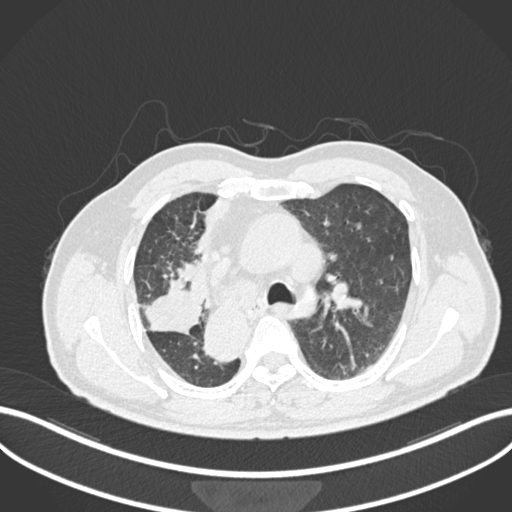
Chest CT, one axial slice; 120 kVp; lung window (W 1500 / L -600 HU); 1 mm slice thickness; 512 × 512 image matrix, field of view 400 × 400 mm. Male patient, age 67 years. Case-level facts recorded for this patient, not image findings: clinical TNM (as recorded): T2a N0 M0.
Annotated regions visible in this slice (rectangle marked by the reading radiologist):
- lung tumour (recorded histology: squamous cell carcinoma): bounding box [x1, y1, x2, y2] px = [138, 272, 206, 337]